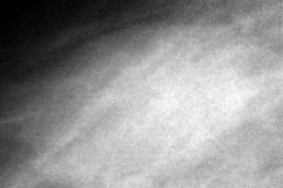
Region of interest cut from a scanned film mammogram (one marked finding), right breast, CC view.
- Finding: mass; BI-RADS assessment category 0 (incomplete: needs additional imaging); pathology (as recorded): benign.